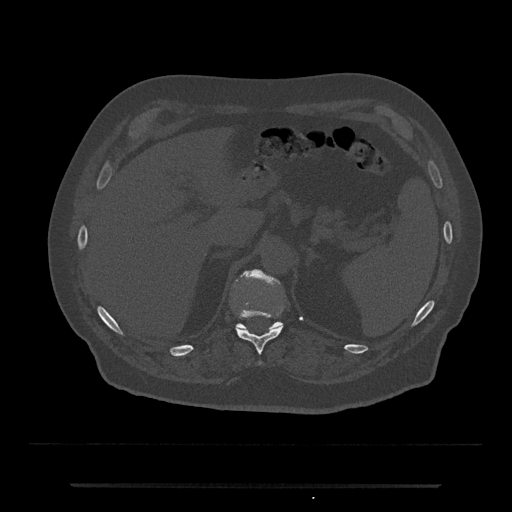
CT including the spine, one axial slice. Position 634 of 797 along the scan axis. Bone window (W 1800 / L 400 HU). 512 × 512 image matrix, field of view 434 × 434 mm. Male patient, age 80 years. From the clinical record (not read from this slice): primary cancer: prostate; vertebrae with lytic lesions (as recorded): L1, T11.
Outlined on this slice (semi-automatic segmentation, software-assisted and operator-edited):
- T11 vertebra: bounding box (x1, y1, x2, y2) in pixels: (236, 311, 283, 365)
- T12 vertebra: (235, 269, 283, 331)